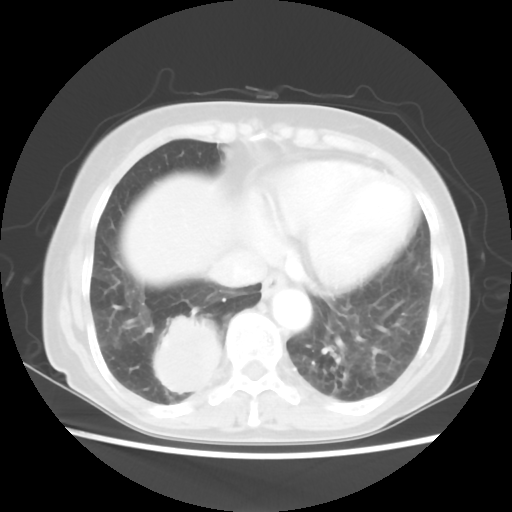
Chest CT, one axial slice; position 19 of 56 along the scan axis; 120 kVp; lung window (W 1500 / L -600 HU); 512 × 512 image matrix. Patient: female, 66 years. From the clinical record (not read from this slice): clinical TNM (as recorded): T2 N3 M0; histopathological grade: G3.
Outlined on this slice (bounding box drawn by a radiologist):
- lung tumour (recorded histology: small cell carcinoma): bounding box (x1, y1, x2, y2) in pixels: (146, 301, 234, 413)